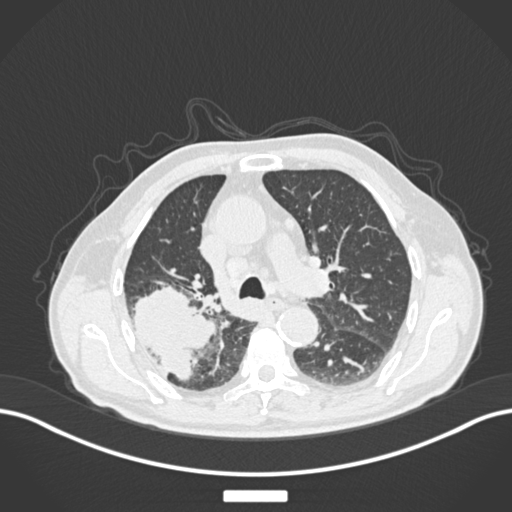
Chest CT, one axial slice; slice 119 of 201 in the series (ordered by position); reconstruction kernel B30f; 120 kVp; lung window (W 1500 / L -600 HU); 1 mm slice thickness; 512 × 512 image matrix, field of view 400 × 400 mm. Male patient, age 72 years. From the clinical record (not read from this slice): clinical TNM (as recorded): T3 N2 M0.
Outlined on this slice (bounding box drawn by a radiologist):
- lung tumour (recorded histology: adenocarcinoma): bounding box <132,273,216,384> (left, top, right, bottom; pixels)